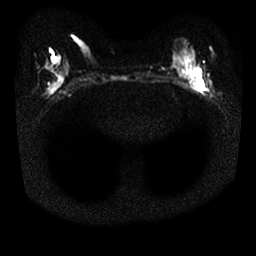
Breast MRI, one axial slice. Slice 11 of 25 in the series (ordered by position). Diffusion-weighted series; image 2 of 4 stored at this slice position (different b-values; order by instance number). 1.5 T. 4 mm slice thickness. 256 × 256 image matrix, field of view 310 × 310 mm. Female patient.
Structures marked on this image (manually delineated by an expert):
- tumour on diffusion-weighted imaging: box from (x=194, y=68) to (x=203, y=91) px